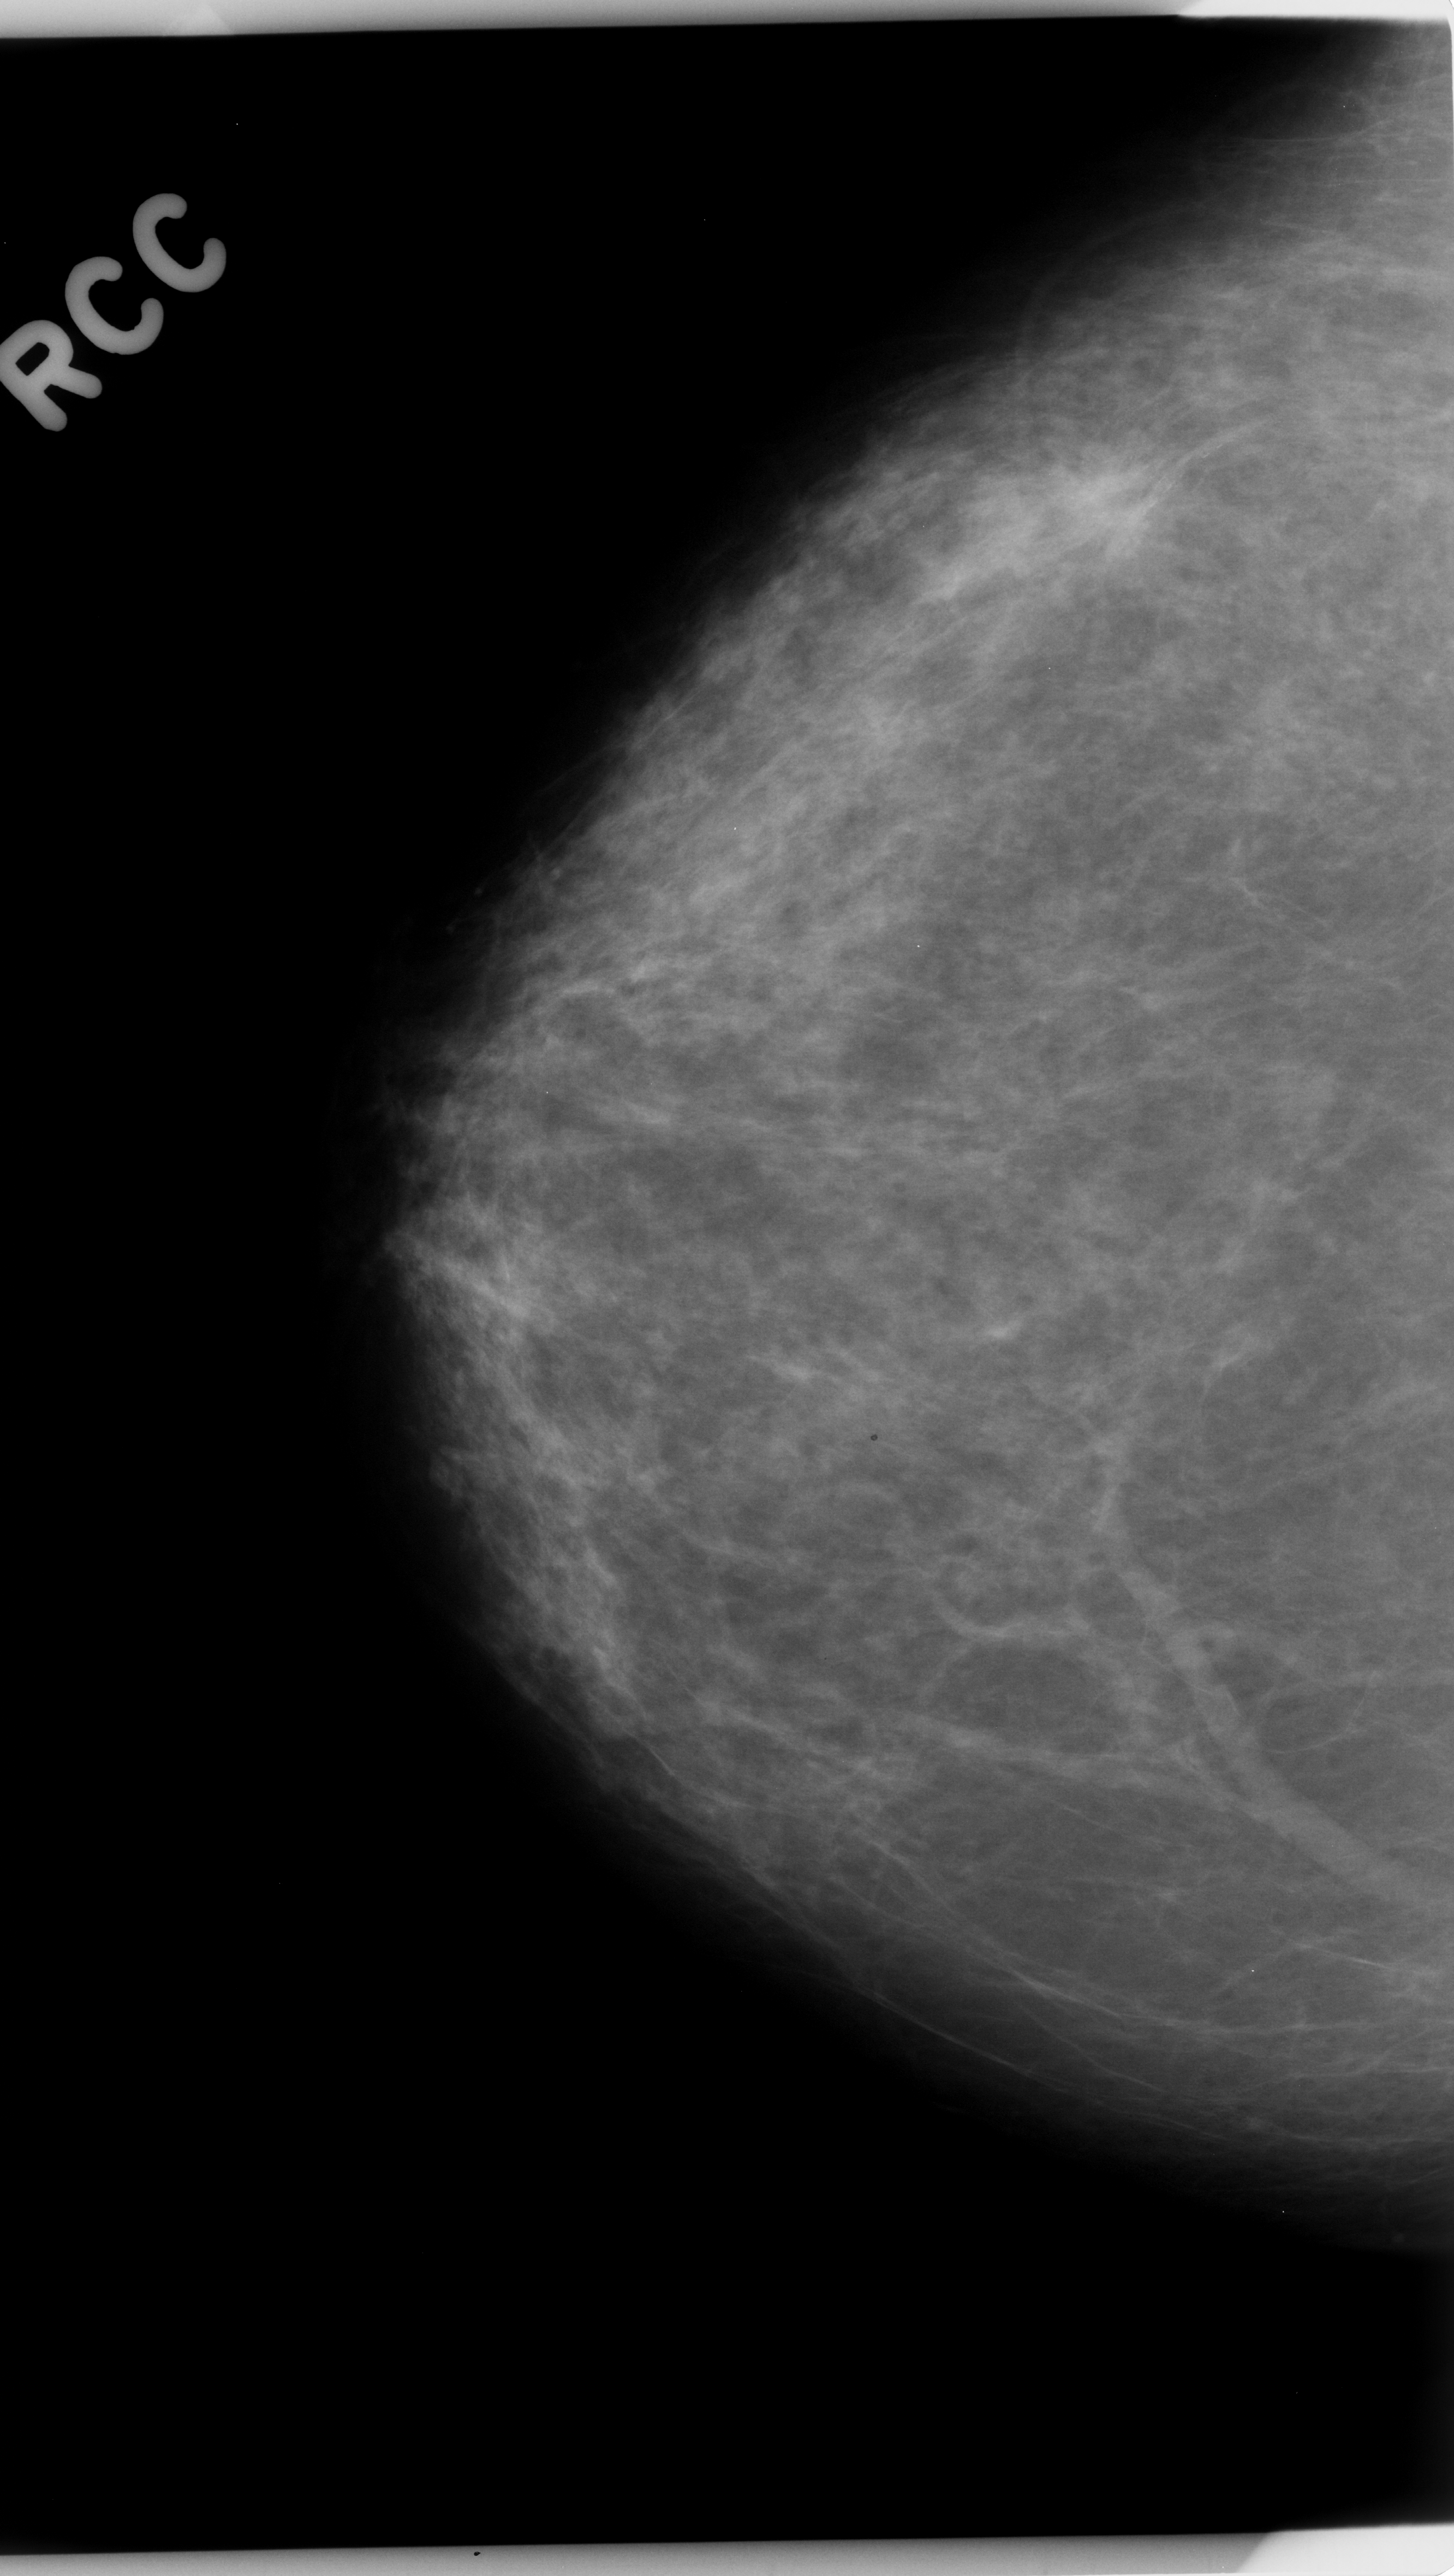
Mammogram (digitized film), right breast, craniocaudal (CC) view.
- Marked findings (only marked abnormalities are described; nothing is implied about the rest of the image): mass, shape irregular, margins spiculated; BI-RADS assessment category 5; subtlety rating 5 on a 1 (subtle) to 5 (obvious) scale; pathology (as recorded): malignant.